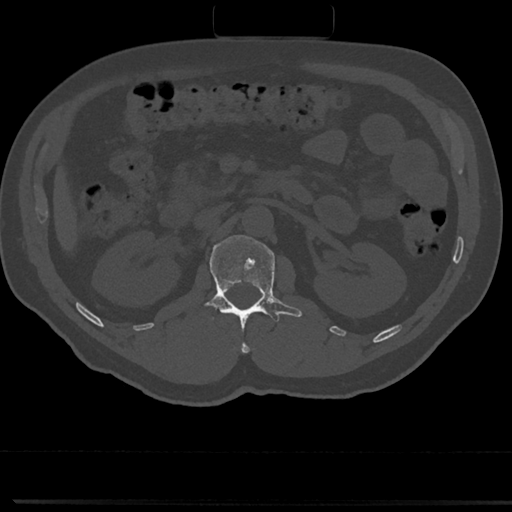
CT including the spine, one axial slice; slice 78 of 817 in the series (ordered by position); 120 kVp; bone window (W 1800 / L 400 HU); 0.5 mm slice thickness; 512 × 512 image matrix, field of view 355 × 355 mm. Male patient, age 61 years. Case-level facts recorded for this patient, not image findings: primary cancer: prostate.
Annotated regions visible in this slice (semi-automatic segmentation, software-assisted and operator-edited):
- L1 vertebra: bounding box (x1, y1, x2, y2) in pixels: (191, 236, 301, 323)